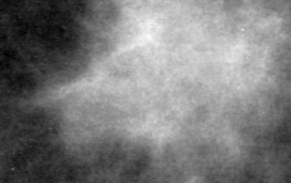
Cropped region of a digitized screen-film mammogram centred on a radiologist-marked abnormality; left breast; MLO view; BI-RADS breast density category 1 (scale 1–4).
Marked abnormality: mass, shape irregular, margins ill defined; BI-RADS assessment category 4; subtlety rating 4 on a 1 (subtle) to 5 (obvious) scale; pathology (as recorded): malignant.